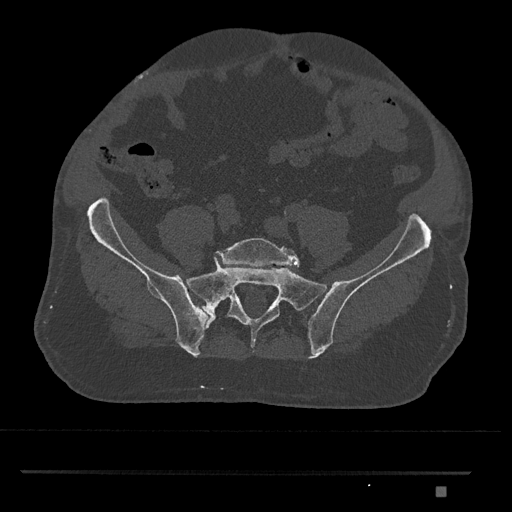
CT including the spine, one axial slice. Position 515 of 1134 along the scan axis. Reconstruction kernel Br40s/3. Bone window (W 1800 / L 400 HU). 0.5 mm slice thickness. 512 × 512 image matrix, field of view 429 × 429 mm. Male patient, age 65 years. From the clinical record (not read from this slice): primary cancer: prostate.
Outlined on this slice (semi-automatically segmented with operator editing):
- L5 vertebra: bounding box [x1, y1, x2, y2] px = [215, 238, 300, 267]